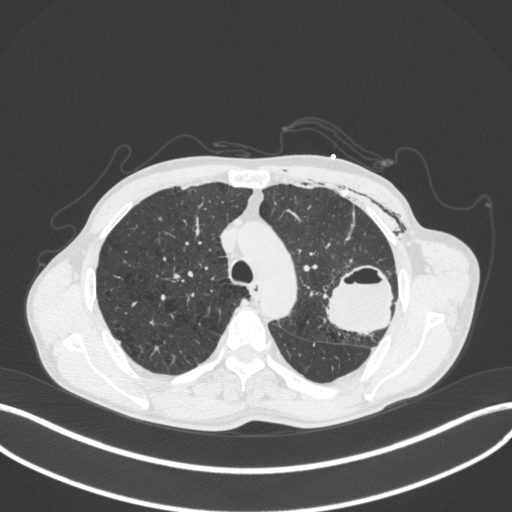
Chest CT, one axial slice. Position 293 of 416 along the scan axis. Reconstruction kernel B31f. Lung window (W 1500 / L -600 HU). 512 × 512 image matrix. Patient: male, 58 years. Case-level facts recorded for this patient, not image findings: clinical TNM (as recorded): T3 N0 M0.
Outlined on this slice (rectangle marked by the reading radiologist):
- lung tumour (recorded histology: adenocarcinoma): bounding box [x1, y1, x2, y2] px = [323, 263, 396, 339]